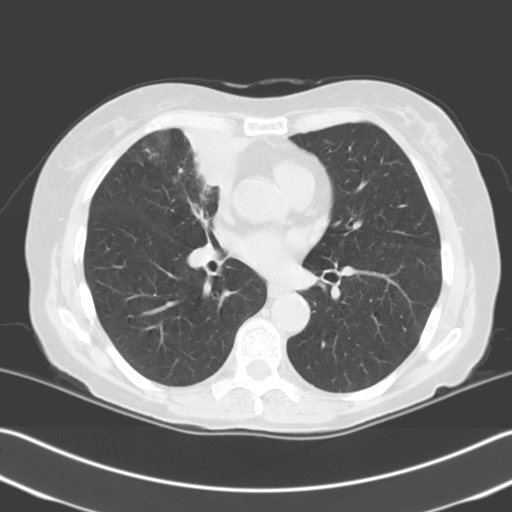
Low-dose screening chest CT, one axial slice; slice 113 of 204 in the series (ordered by position); 140 kVp; lung window (W 1500 / L -600 HU); 512 × 512 image matrix.
Outlined on this slice (expert manual segmentation):
- lesion 1 (tumor, upper lobe of right lung): box from (x=185, y=131) to (x=249, y=188) px